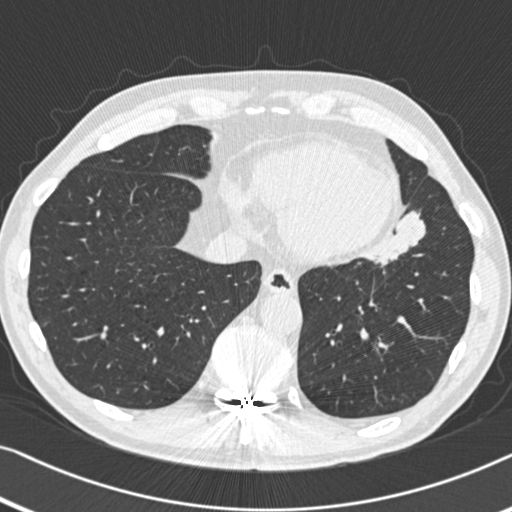
Low-dose screening chest CT, one axial slice; slice 132 of 383 in the series (ordered by position); reconstruction kernel B30f; lung window (W 1500 / L -600 HU); 1 mm slice thickness; 512 × 512 image matrix.
Annotated regions visible in this slice (manually delineated by an expert):
- lesion 1 (tumor, upper lobe of left lung): bounding box [x1, y1, x2, y2] px = [376, 211, 426, 266]